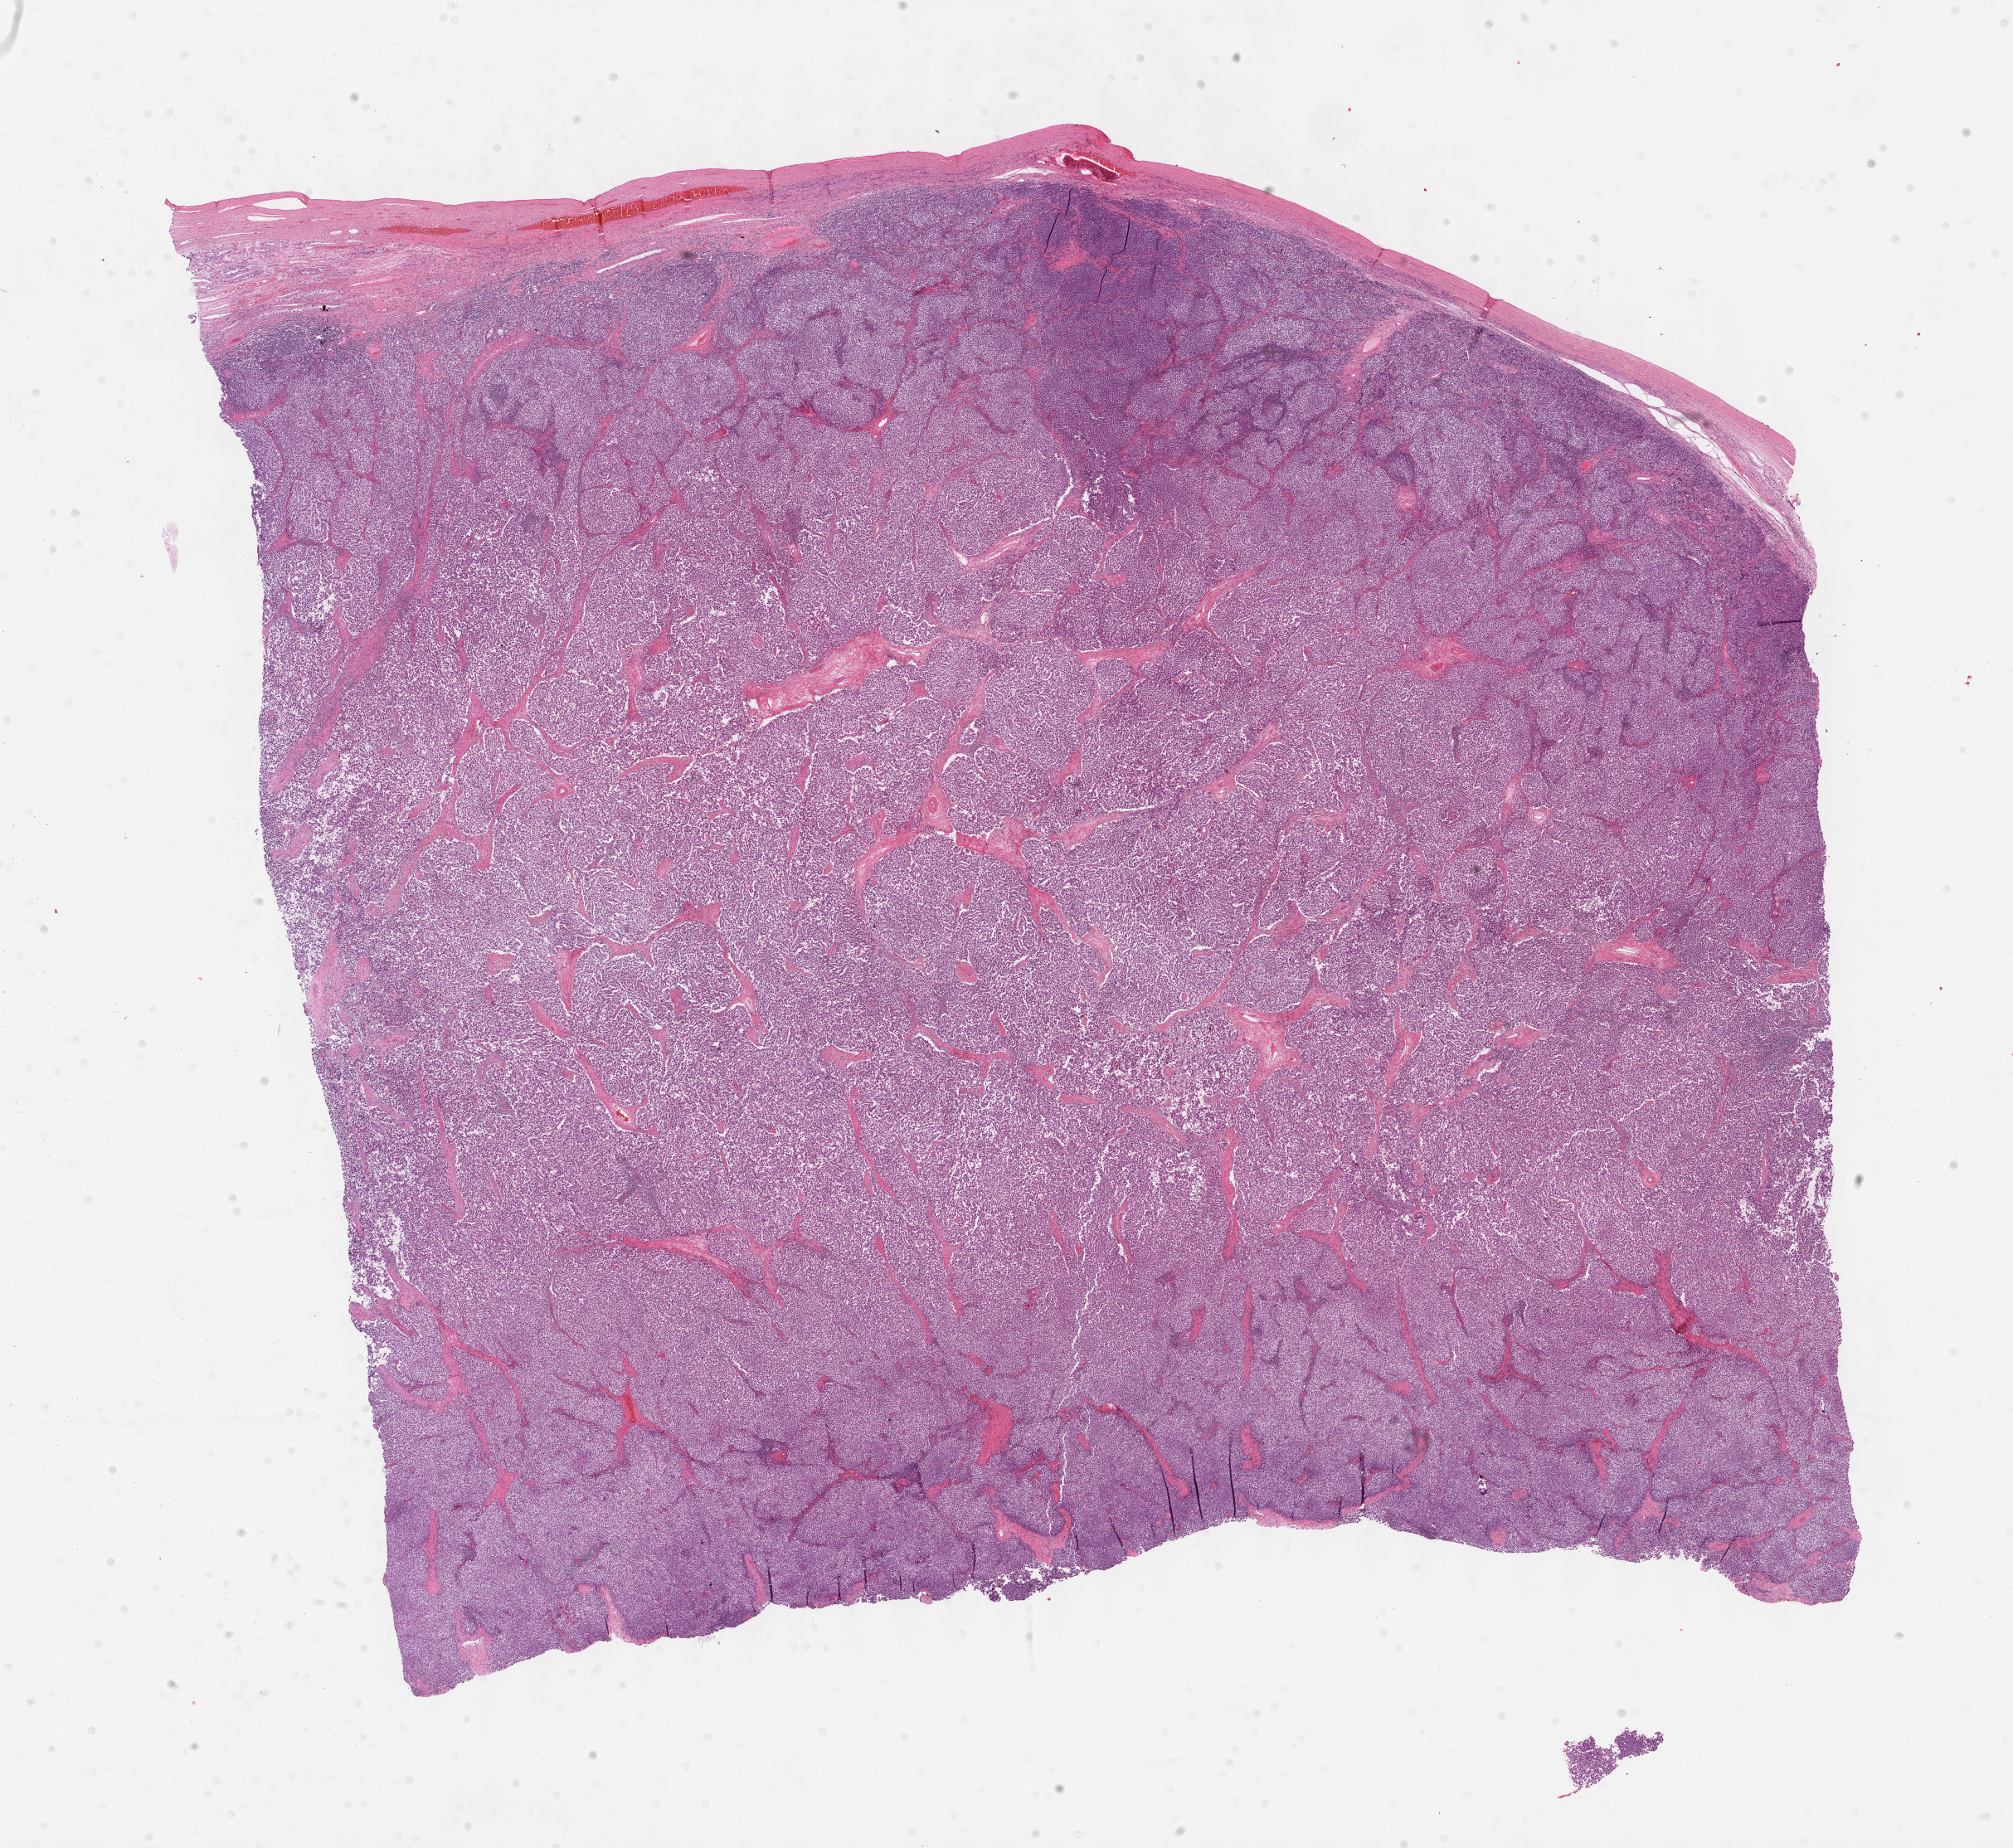
H&E-stained whole-slide image, whole scanned area (about 19.6 x 18.0 mm, slide scanned at 40x) shown as a low-resolution overview, FFPE section, testis, primary tumour sample. Male patient; age at initial diagnosis 38 years.
* pathologic diagnosis: Seminoma, NOS